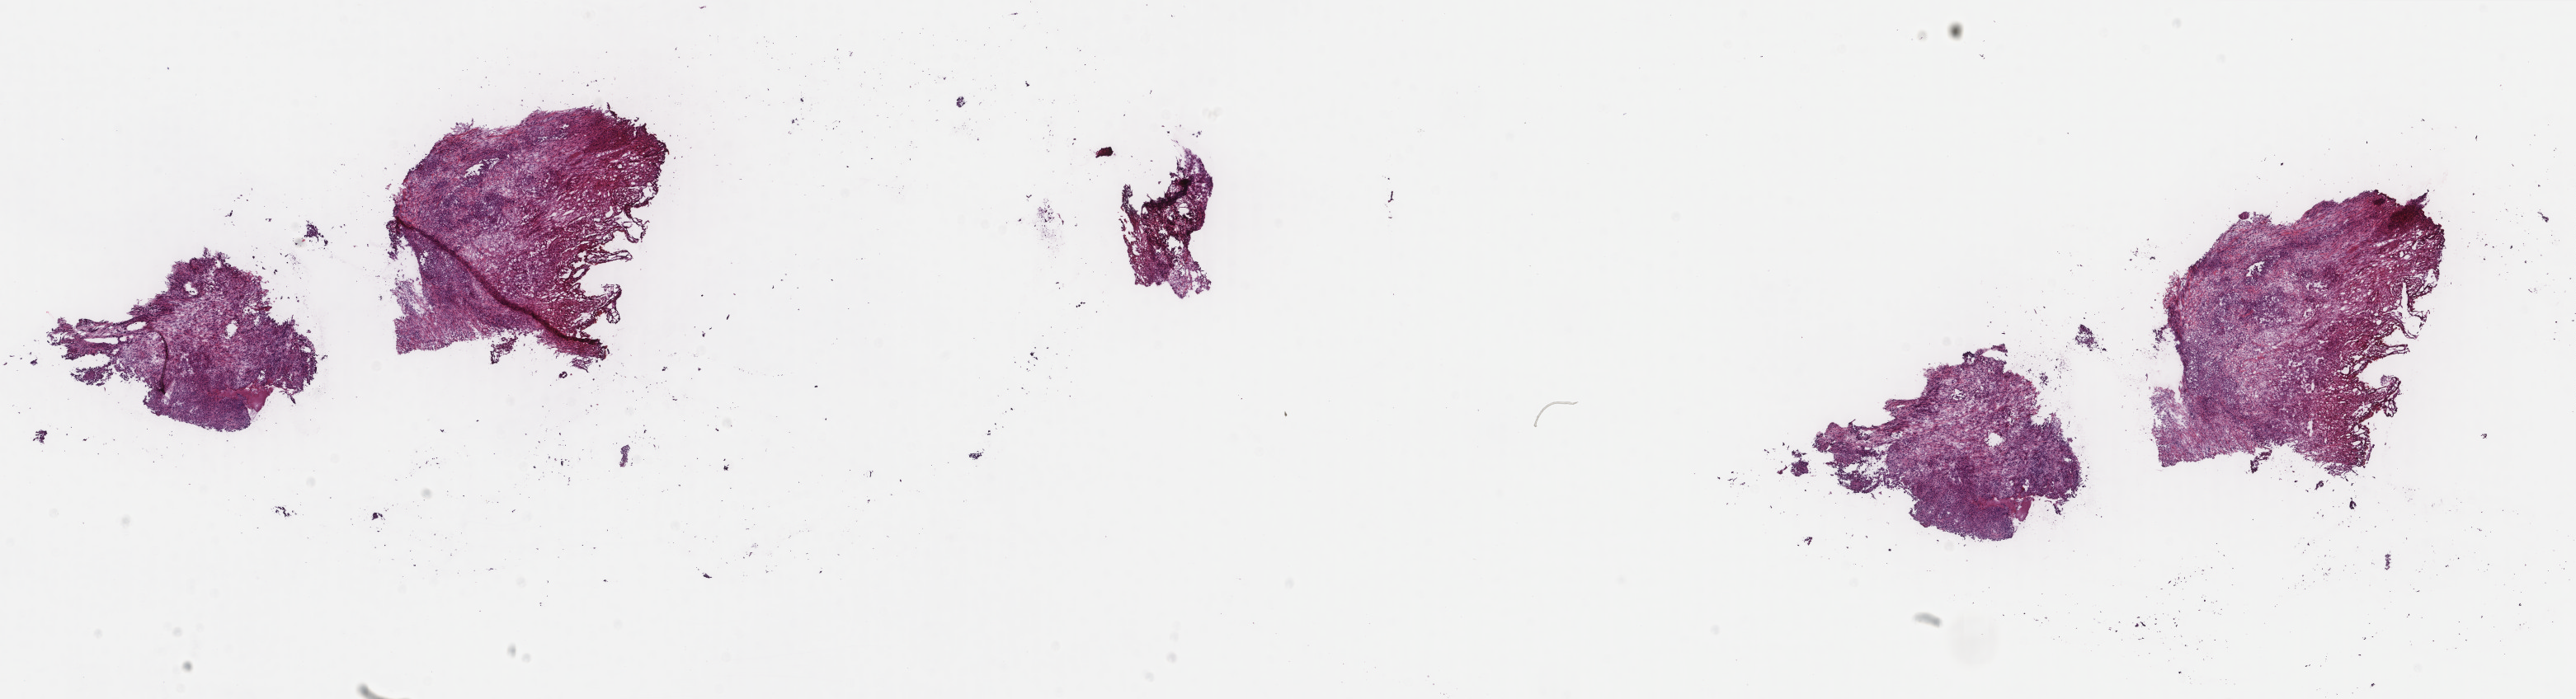
Digitized H&E-stained tissue section (whole slide) — a low-resolution overview of the entire scanned area, about 24.8 x 6.7 mm, frozen section from the top of the tissue portion, primary tumour sample from the bladder. Patient: female, age at initial diagnosis 67 years.
Diagnosis: Transitional cell carcinoma (lateral wall of bladder).